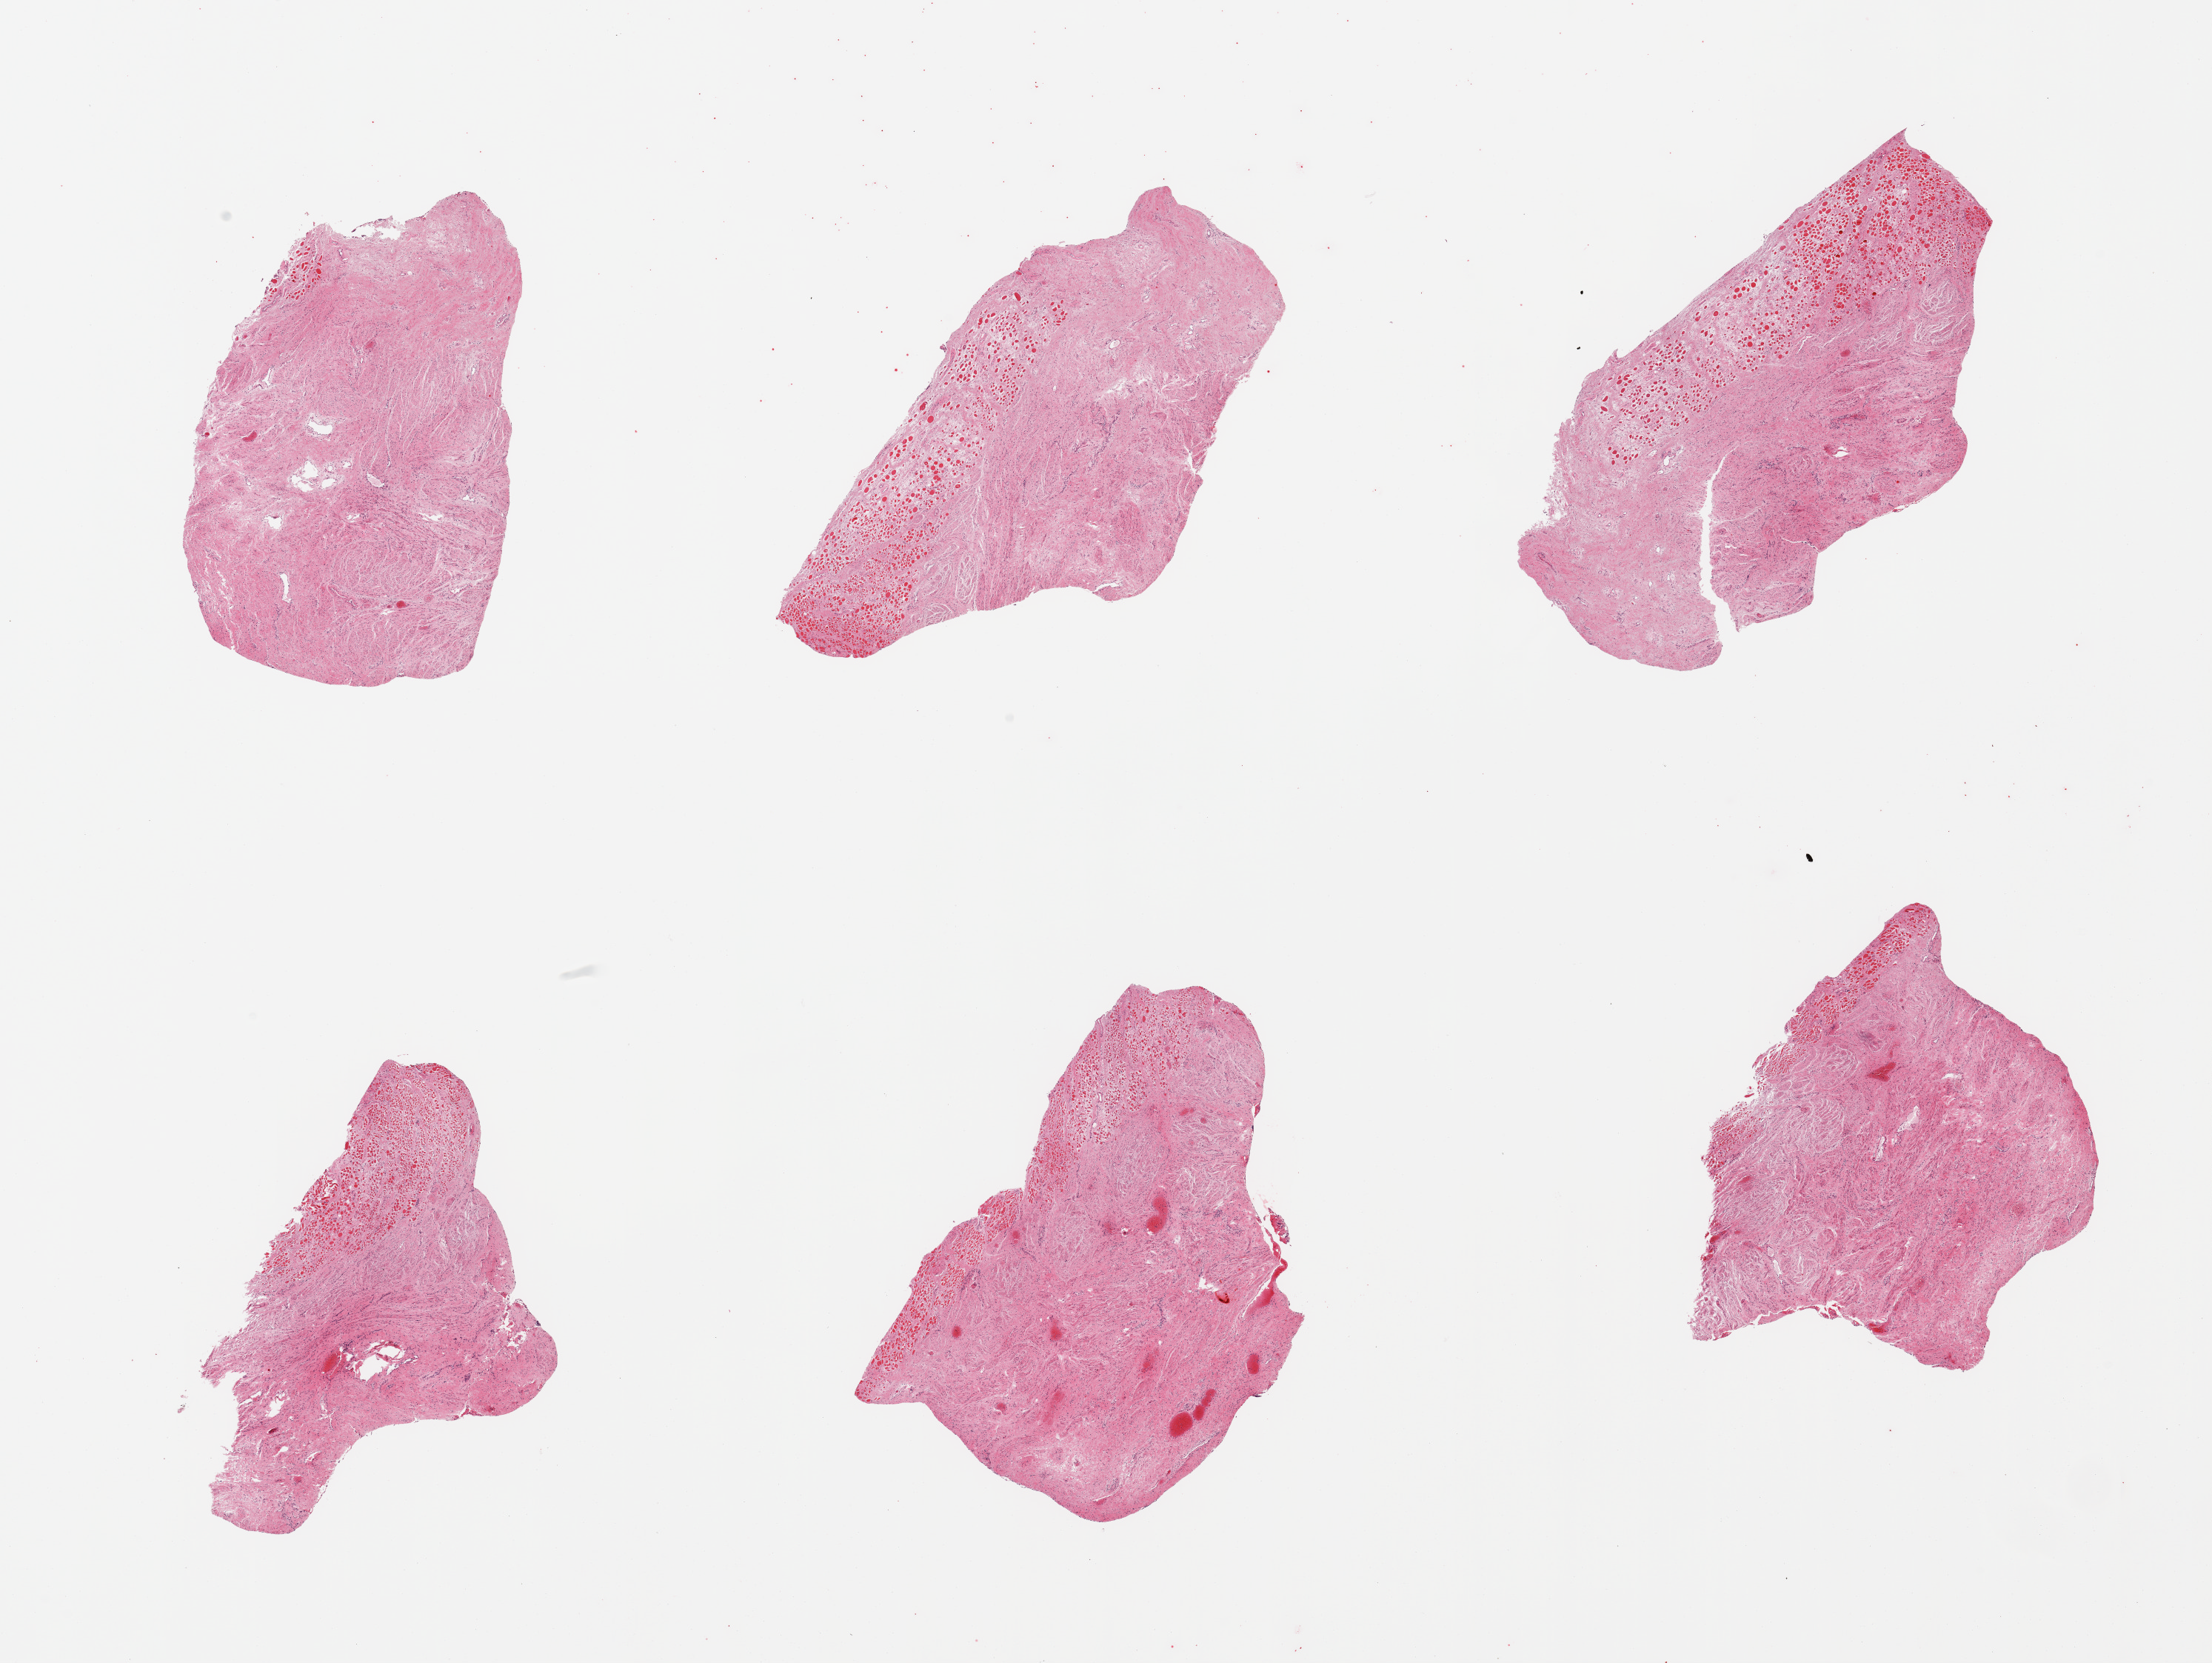
Digitized haematoxylin and eosin-stained section, shown as a low-resolution overview of the whole scanned area (about 23.6 x 17.8 mm). PAXgene-fixed, paraffin-embedded tissue. Sampled site (target tissue): vagina. Donor tissue sample.
Review note (as recorded): 6 pieces; congested fibromuscular stroma and skeletal muscle fragments only in this section.